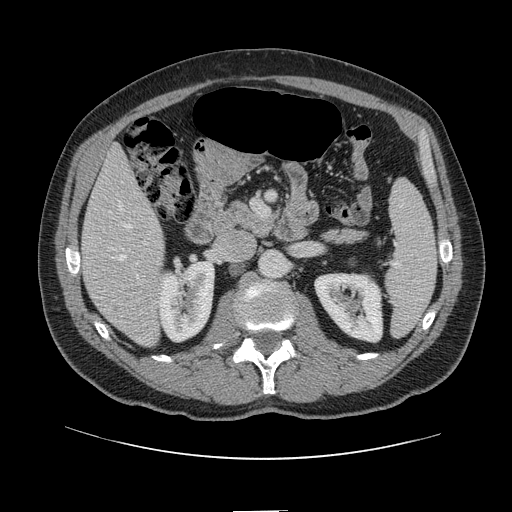
Contrast-enhanced abdominal CT, one axial slice; position 48 of 161 along the scan axis; 120 kVp; intravenous contrast given; soft-tissue window (W 400 / L 40 HU); 2.5 mm slice thickness; 512 × 512 image matrix. Male patient, age 66 years. From the clinical record (not read from this slice): diagnosis: colorectal cancer liver metastases, imaged before liver resection; multiple liver metastases: no; largest metastasis: 3.5 cm; disease in both lobes: no.
Outlined on this slice (manually delineated by an expert):
- hepatic veins: box from (x=120, y=204) to (x=131, y=260) px
- liver: (x=82, y=150)–(x=163, y=346)
- planned liver remnant (the part of the liver to remain after resection): (x=81, y=150)–(x=158, y=275)